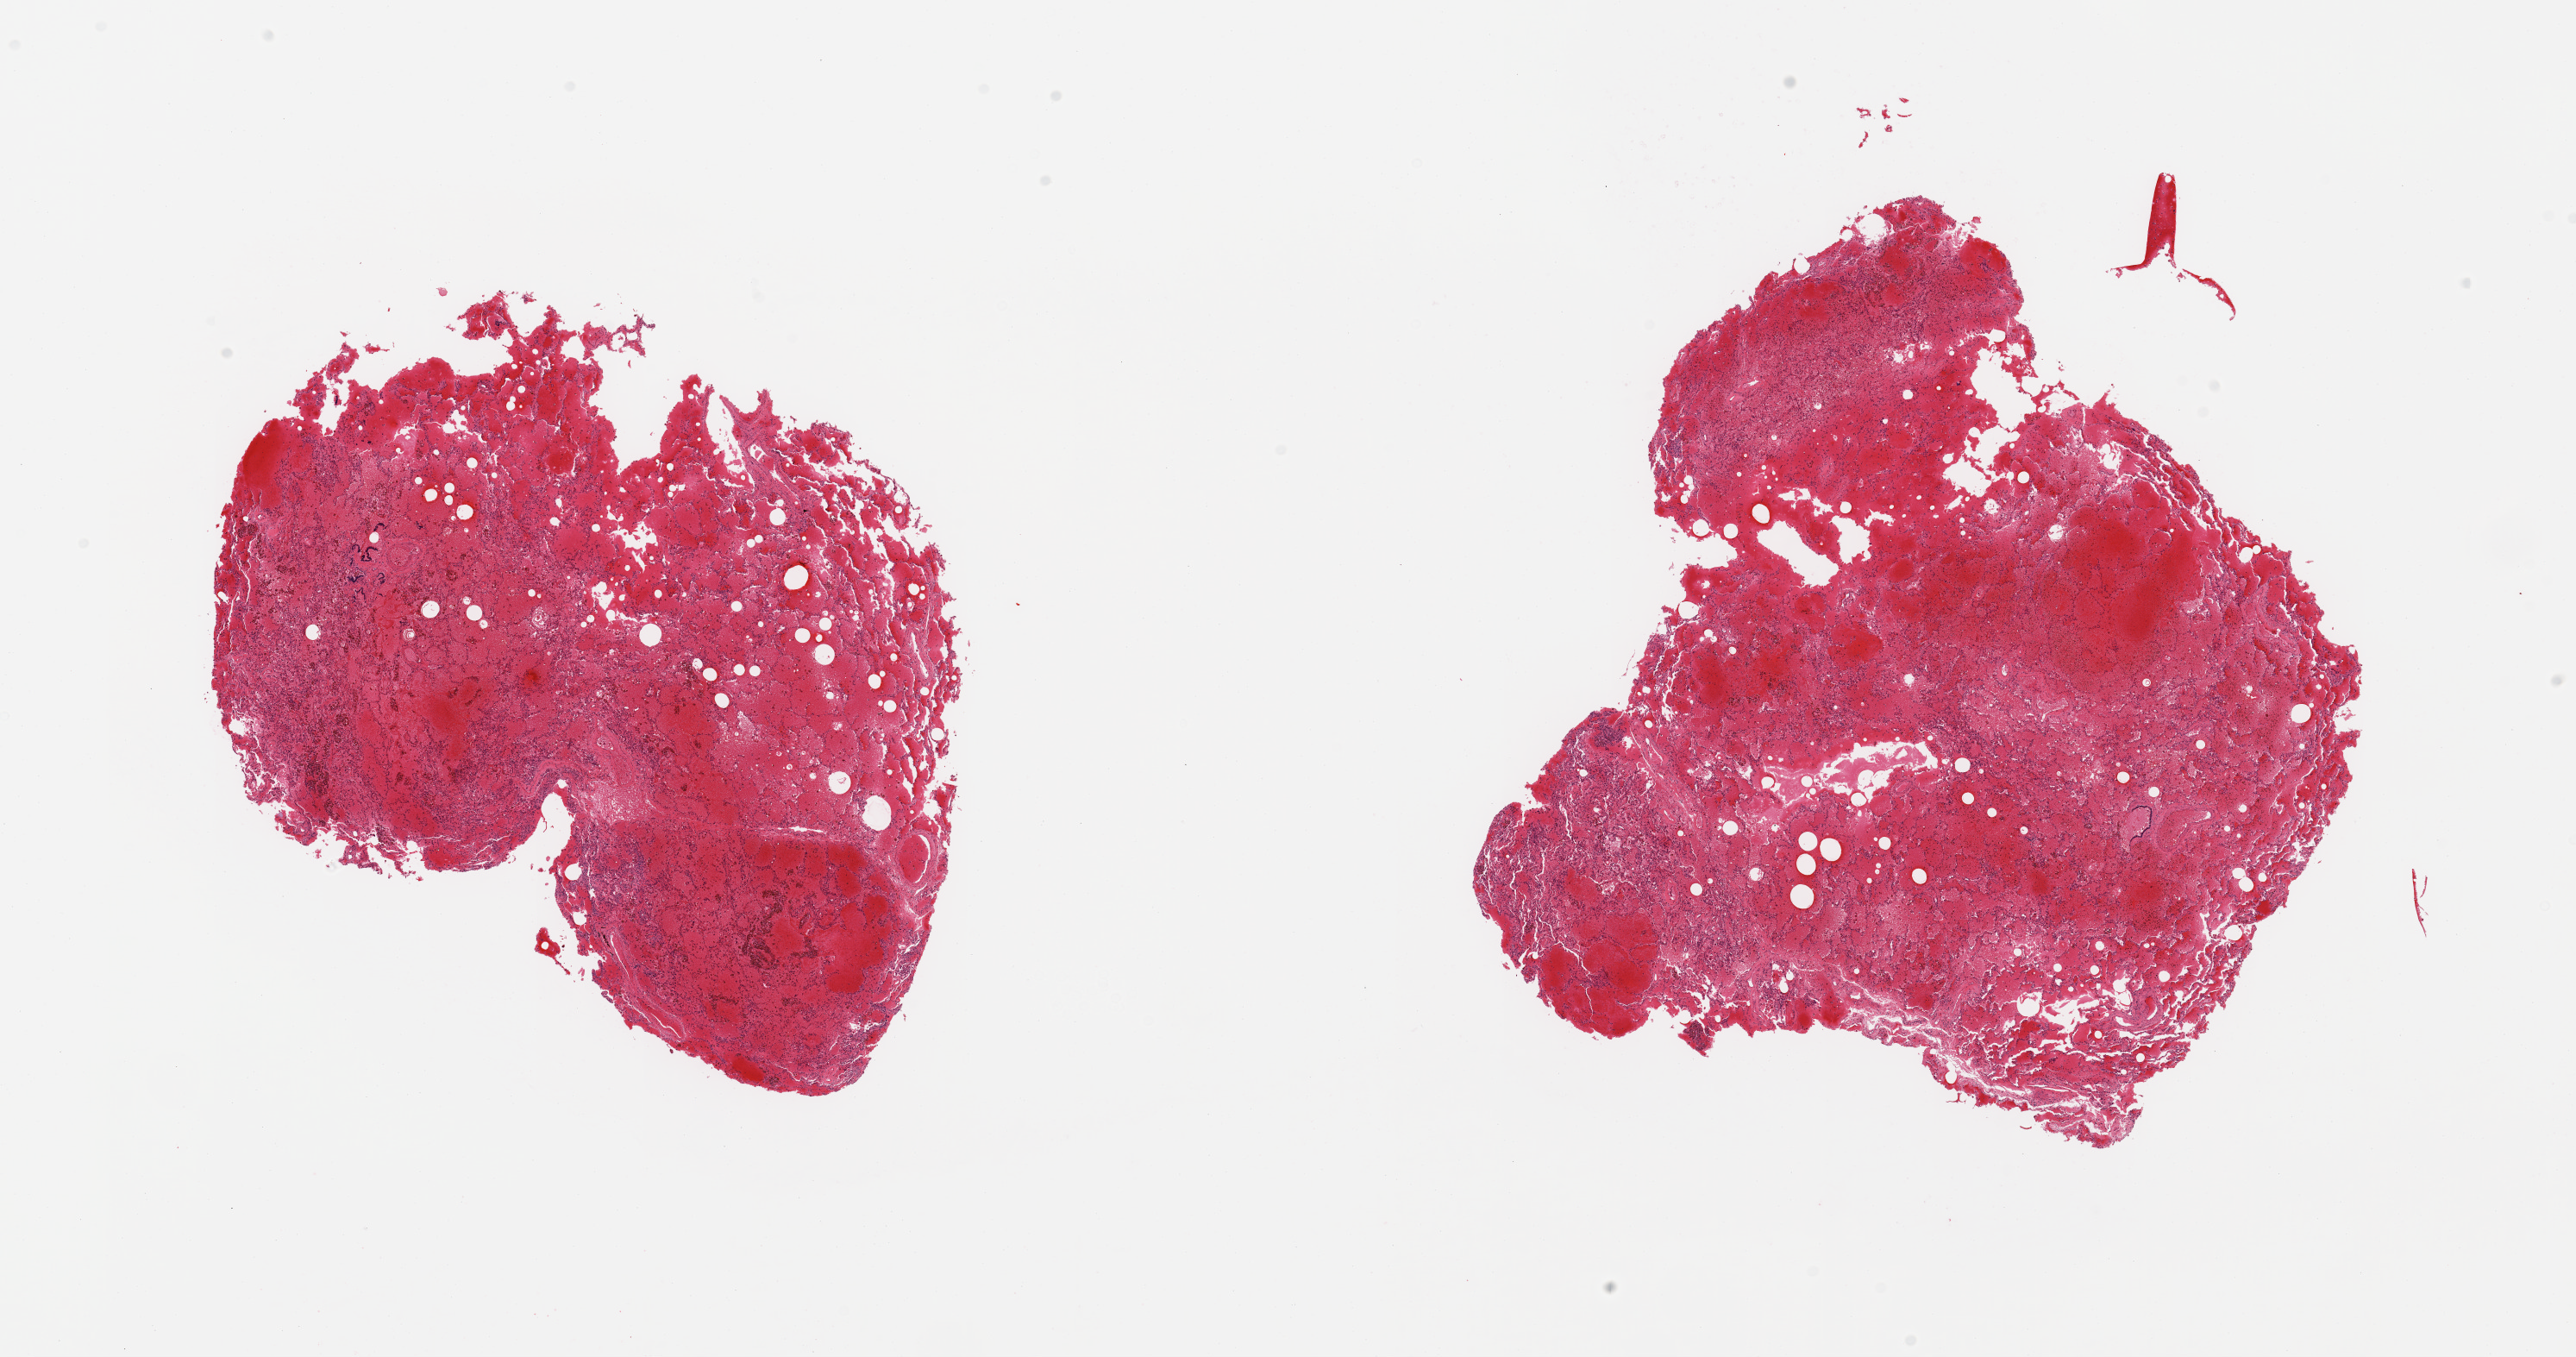
Haematoxylin and eosin whole-slide image, brightfield, low-resolution overview of the scanned area, about 23.6 x 12.4 mm. PAXgene-fixed, paraffin-embedded tissue. Sampled site (target tissue): lung. Tissue donor sample. Male donor.
Pathologist's review note for this sample: 2 pieces, diffuse congestion, acute and chronic.